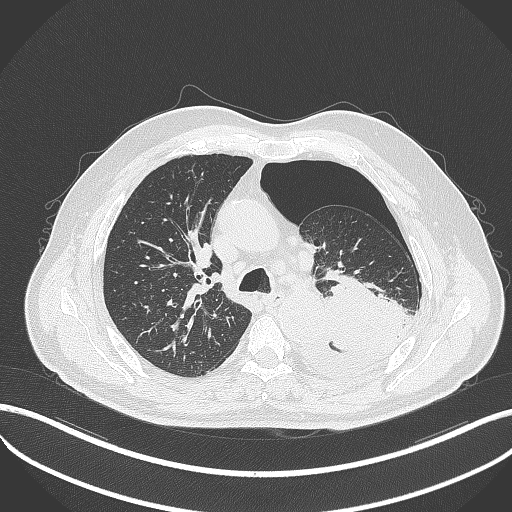
Chest CT, one axial slice; position 348 of 464 along the scan axis; reconstruction kernel B70f; 120 kVp; lung window (W 1500 / L -600 HU); 1 mm slice thickness; 512 × 512 image matrix, field of view 400 × 400 mm. Patient: male, 76 years. From the clinical record (not read from this slice): clinical TNM (as recorded): T3 N0 M1b.
Outlined on this slice (rectangle marked by the reading radiologist):
- lung tumour (recorded histology: adenocarcinoma): box from (x=317, y=267) to (x=410, y=350) px